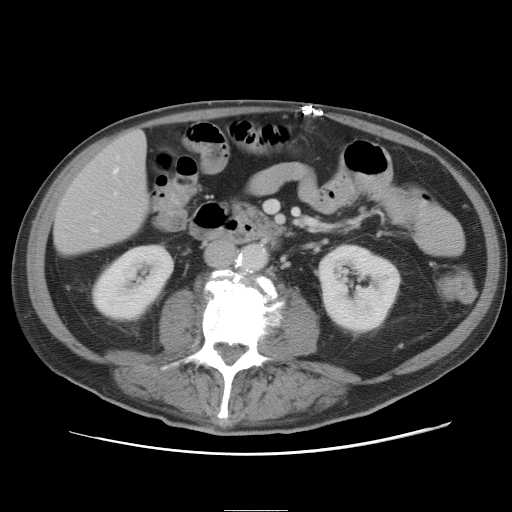
Contrast-enhanced abdominal CT, one axial slice. Slice 13 of 89 in the series (ordered by position). 120 kVp. Intravenous contrast given. Soft-tissue window (W 400 / L 40 HU). 5 mm slice thickness. 512 × 512 image matrix, field of view 375 × 375 mm. Male patient, age 69 years. Case-level facts recorded for this patient, not image findings: diagnosis: colorectal cancer liver metastases, imaged before liver resection; multiple liver metastases: no; largest metastasis: 8.5 cm; chemotherapy before resection: no.
Outlined on this slice (manually delineated by an expert):
- hepatic veins: bounding box <95,156,119,231> (left, top, right, bottom; pixels)
- liver: <56,132,150,255>
- planned liver remnant (the part of the liver to remain after resection): <55,132,149,255>